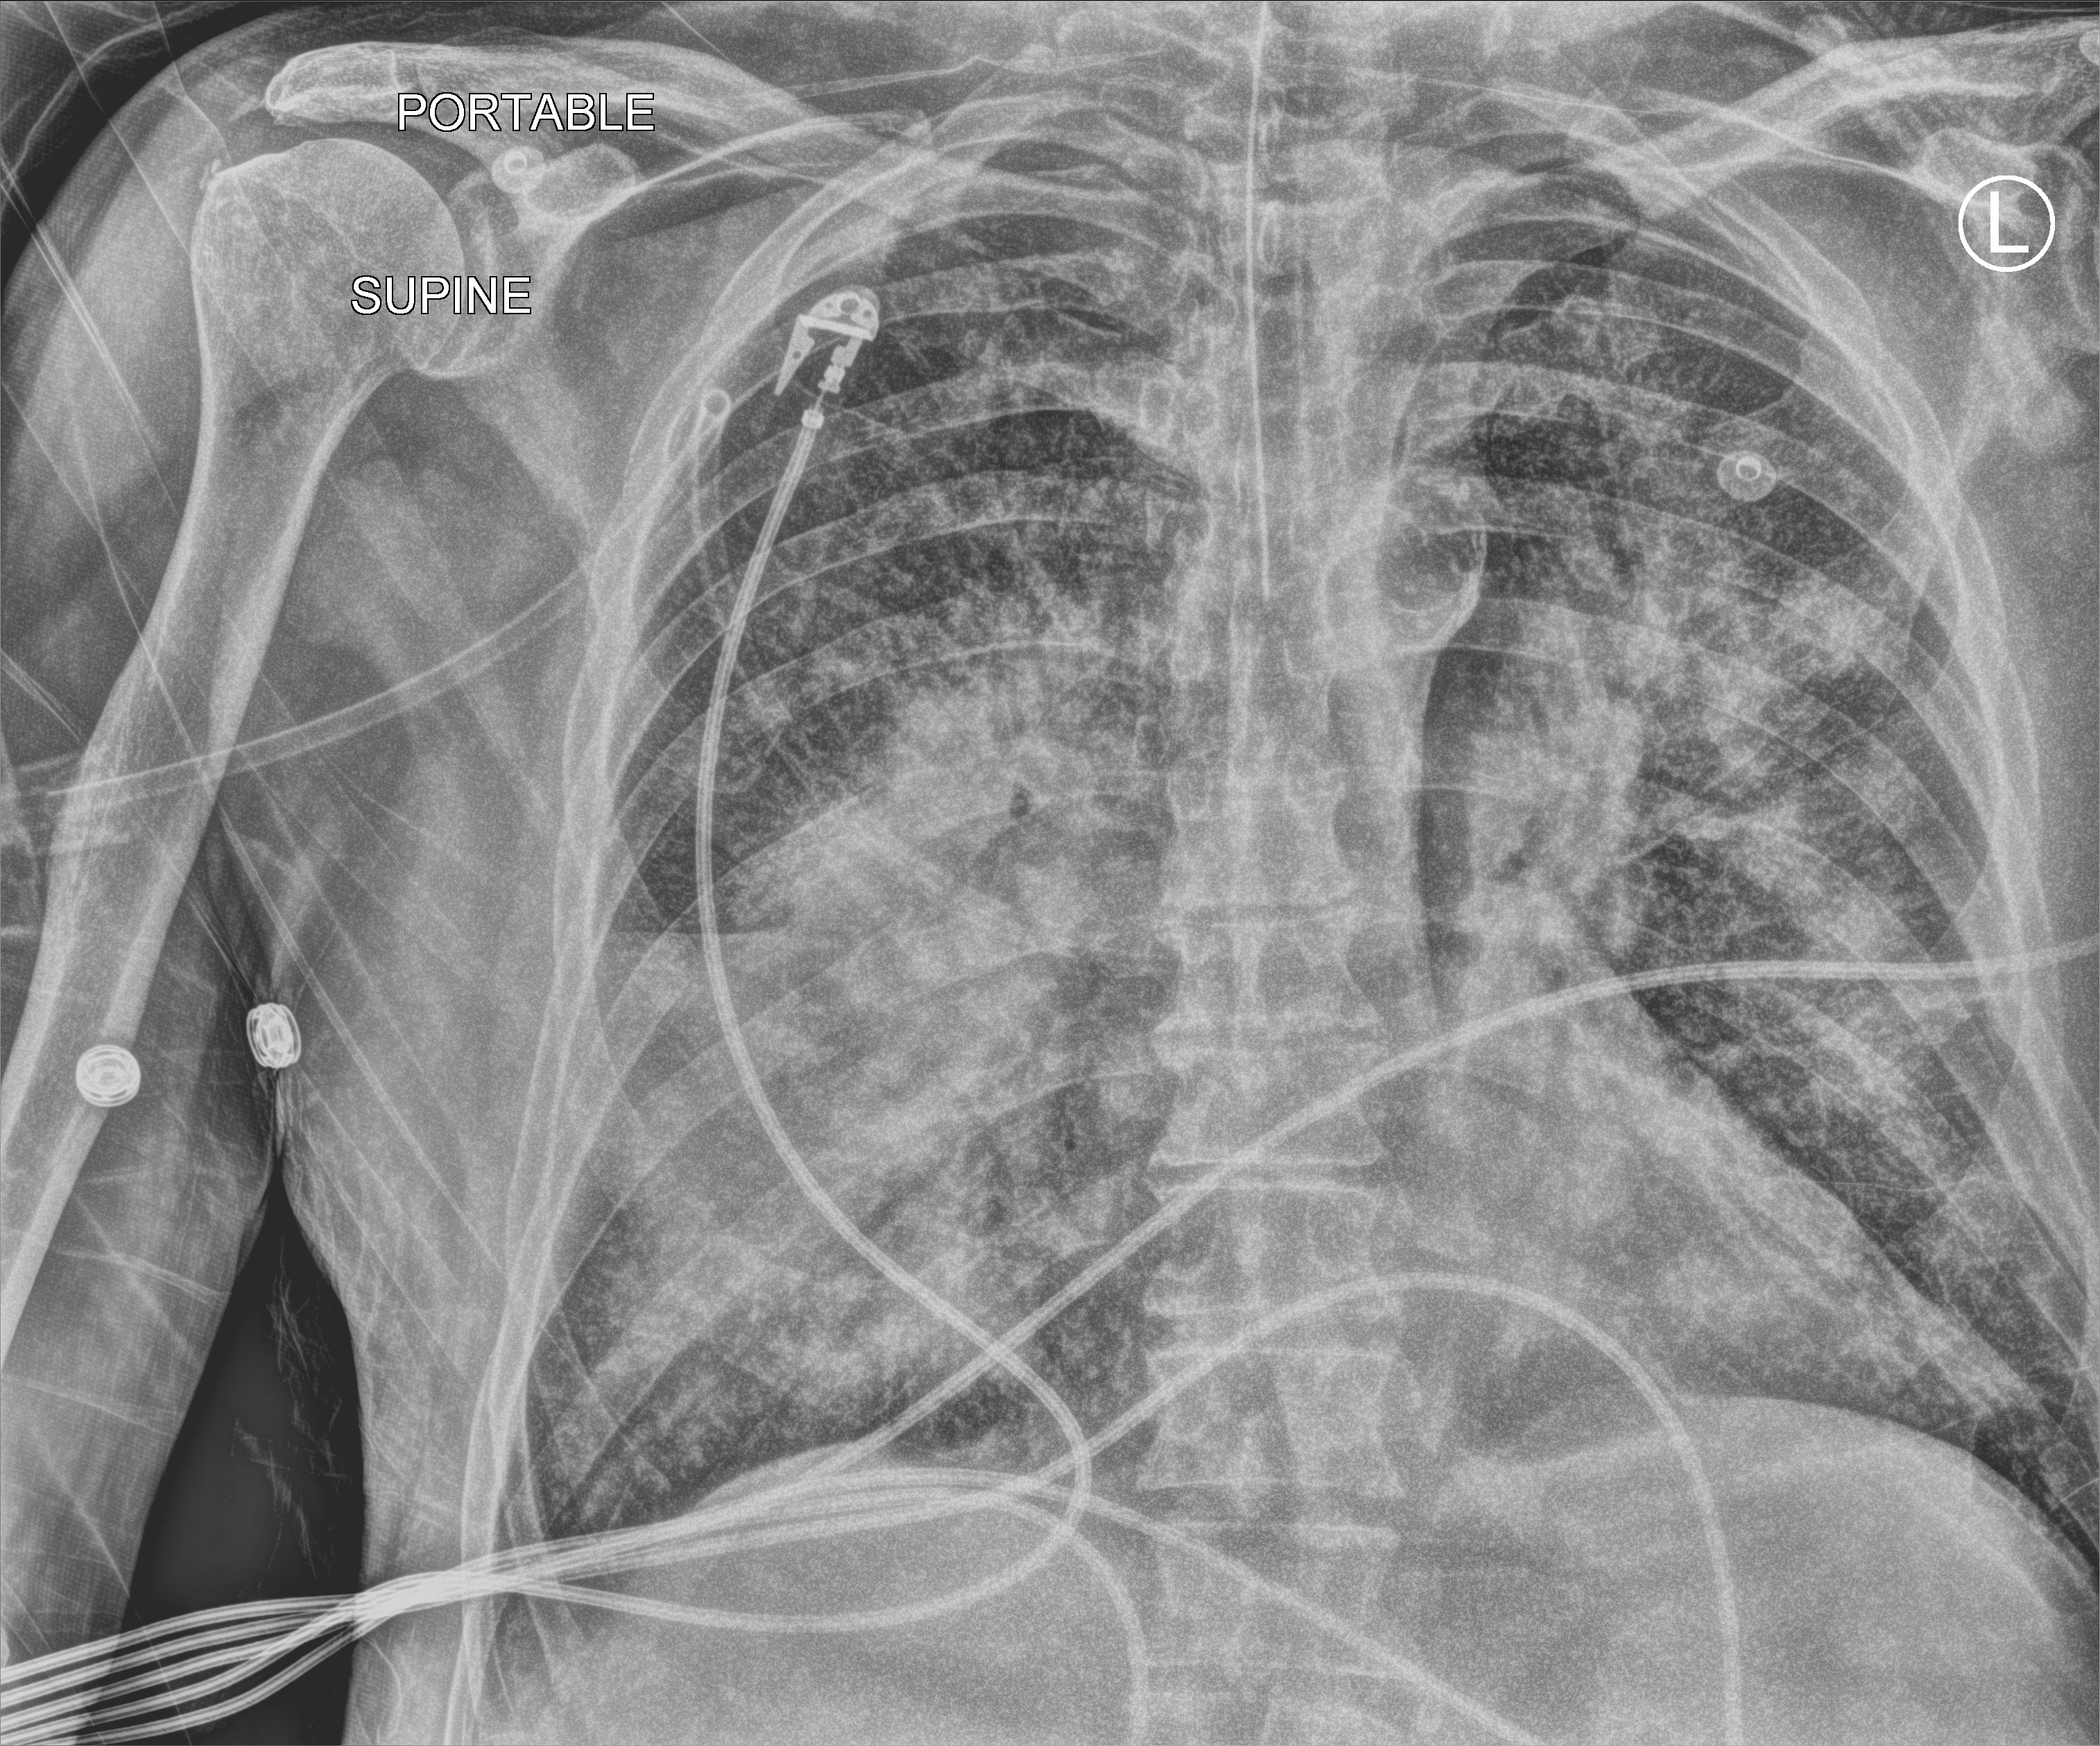
Portable chest radiograph; anteroposterior (AP) projection. Male patient hospitalised with COVID-19, age 60–74 years.
Hospital-stay facts (about this admission, not read from this image; timing relative to this image not recorded): mechanically ventilated during this hospital stay: yes; admitted to intensive care during this hospital stay: yes.